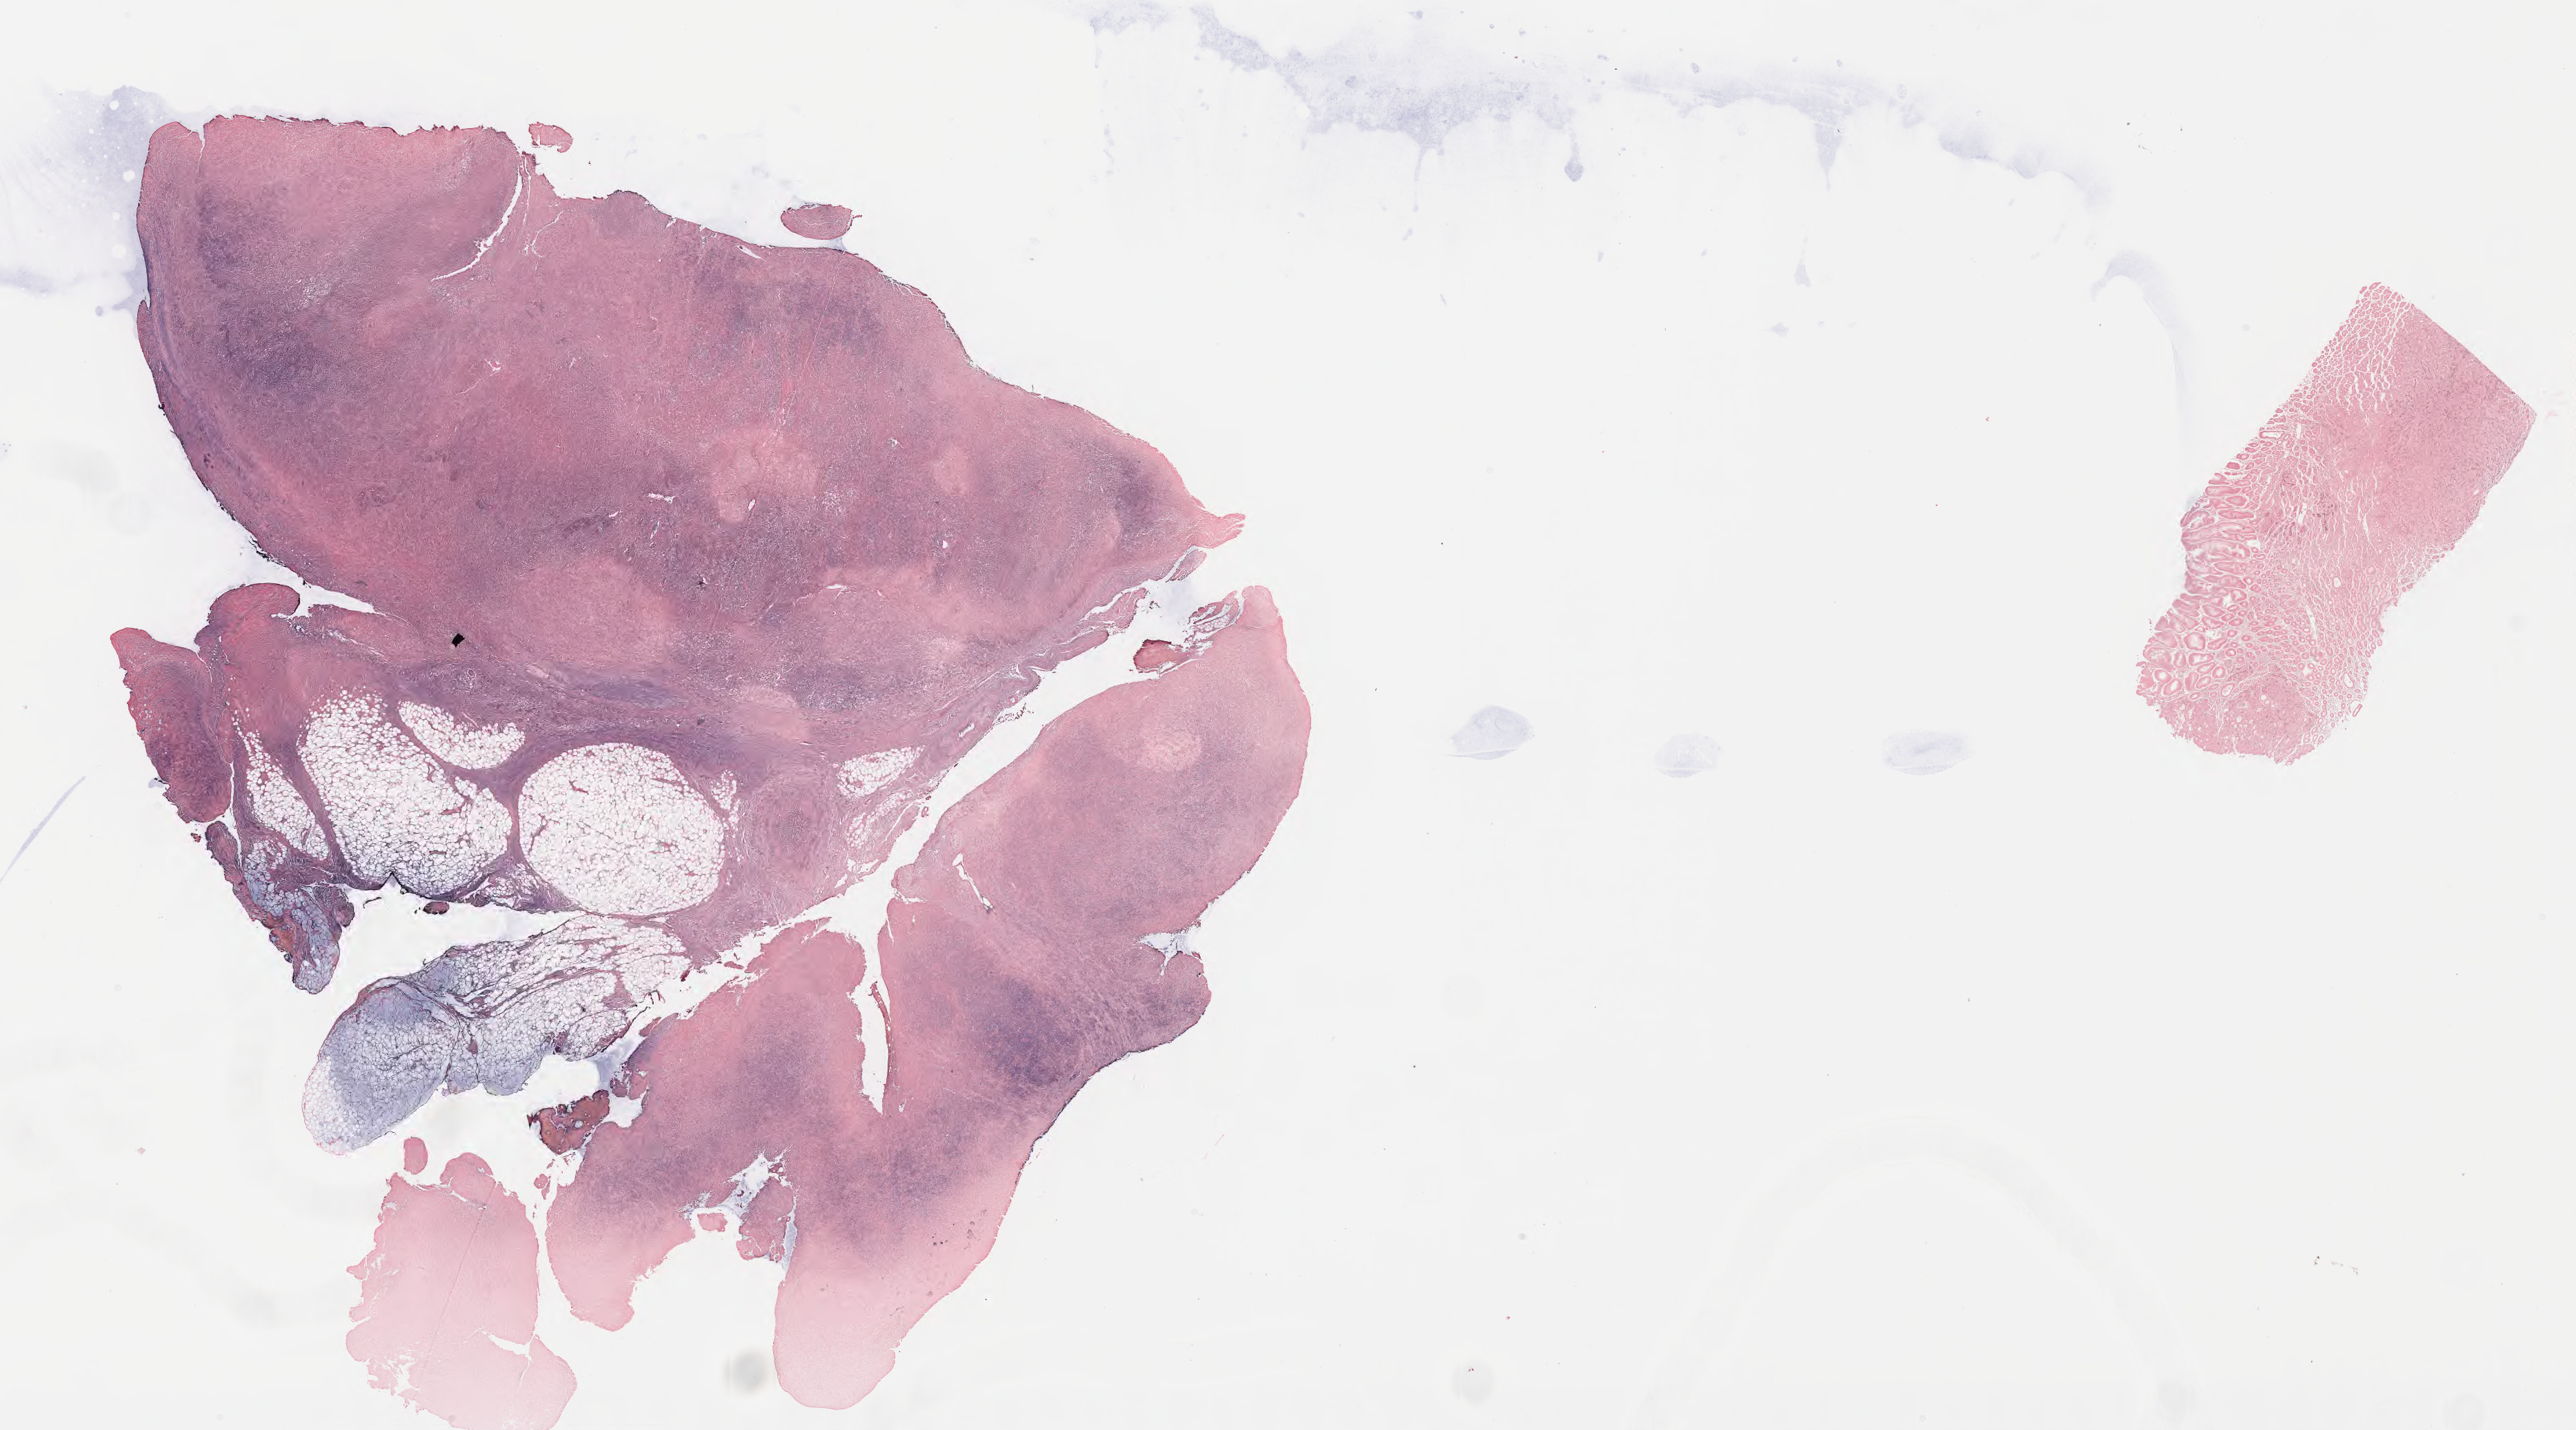
Whole-slide image, Epstein–Barr virus-encoded RNA (EBER) in-situ hybridisation — whole scanned area (about 30.2 x 16.8 mm) shown as a low-resolution overview. Tumor tissue. Patient female; aged 46.
Diagnosis: Diffuse large B-cell lymphoma, NOS.